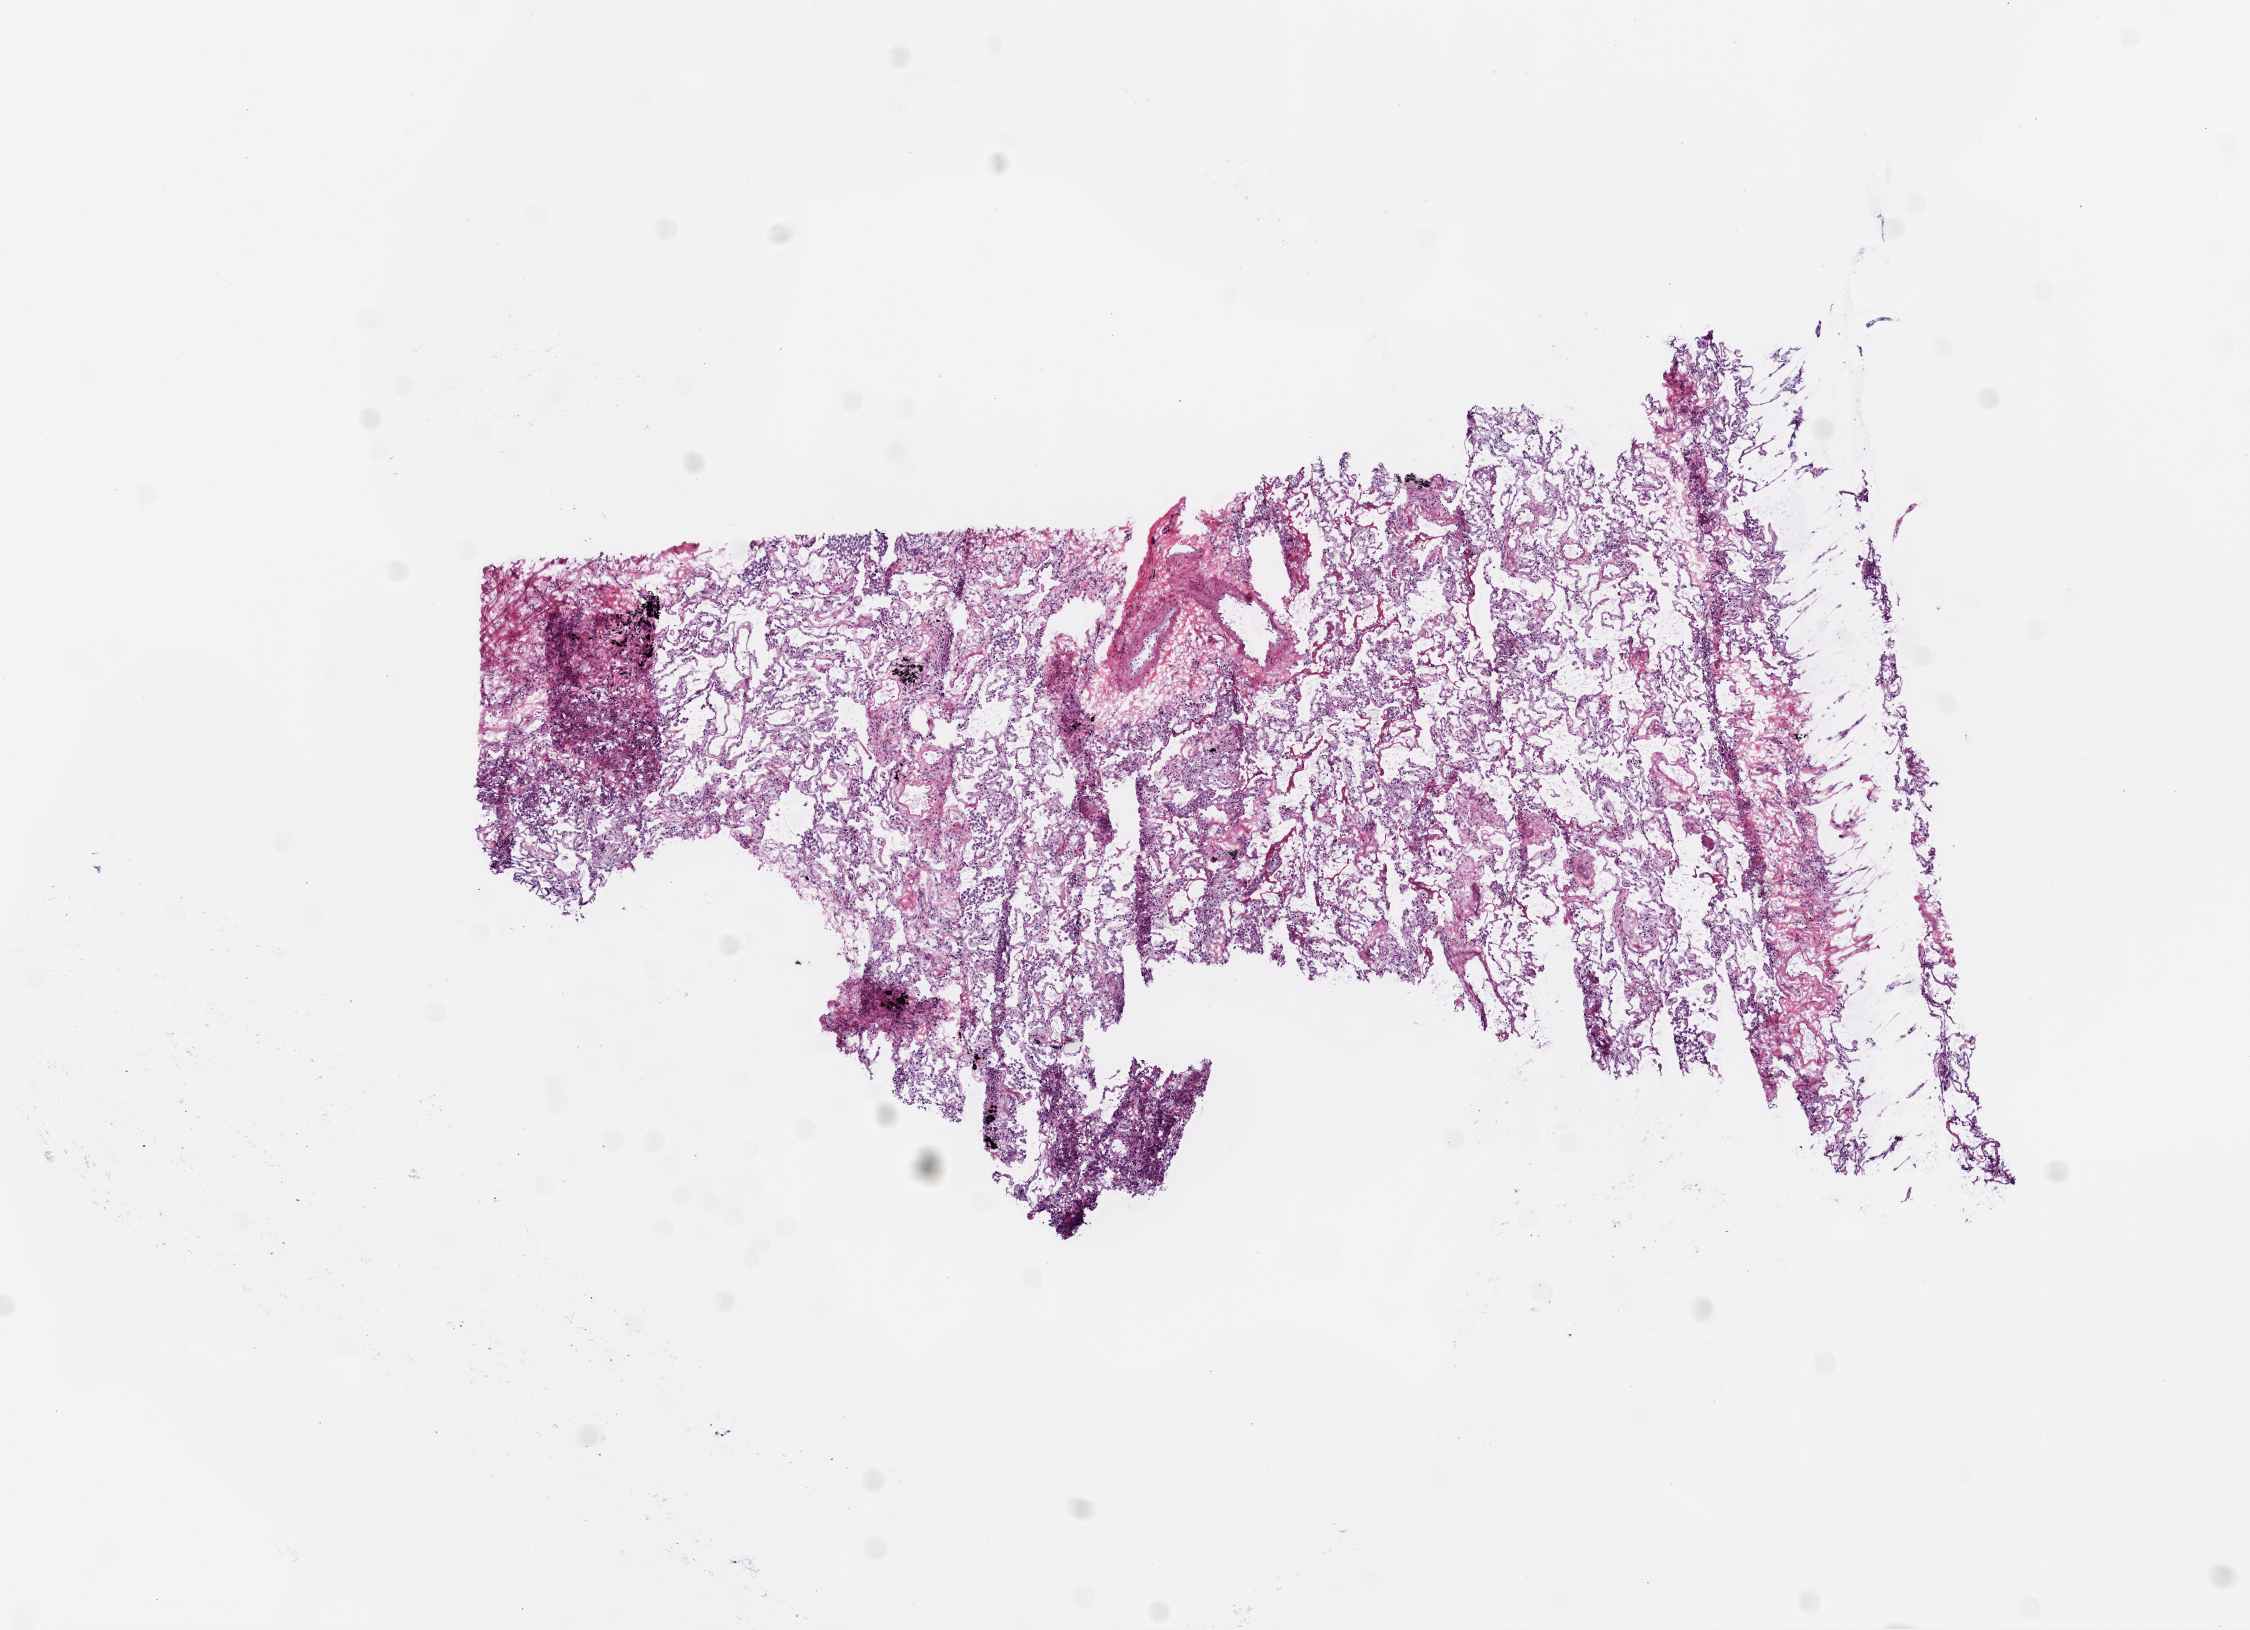
Digitized H&E-stained tissue section (whole slide) — shown as a low-resolution overview of the whole scanned area (about 9.0 x 6.5 mm, from a 20x scan), frozen section, sample: solid tissue normal (non-tumour tissue), lung. Patient: male, age at initial diagnosis 77 years.
This section: solid tissue normal (non-tumour) sample from the same patient. Patient diagnosis: Squamous cell carcinoma, NOS (upper lobe, lung).